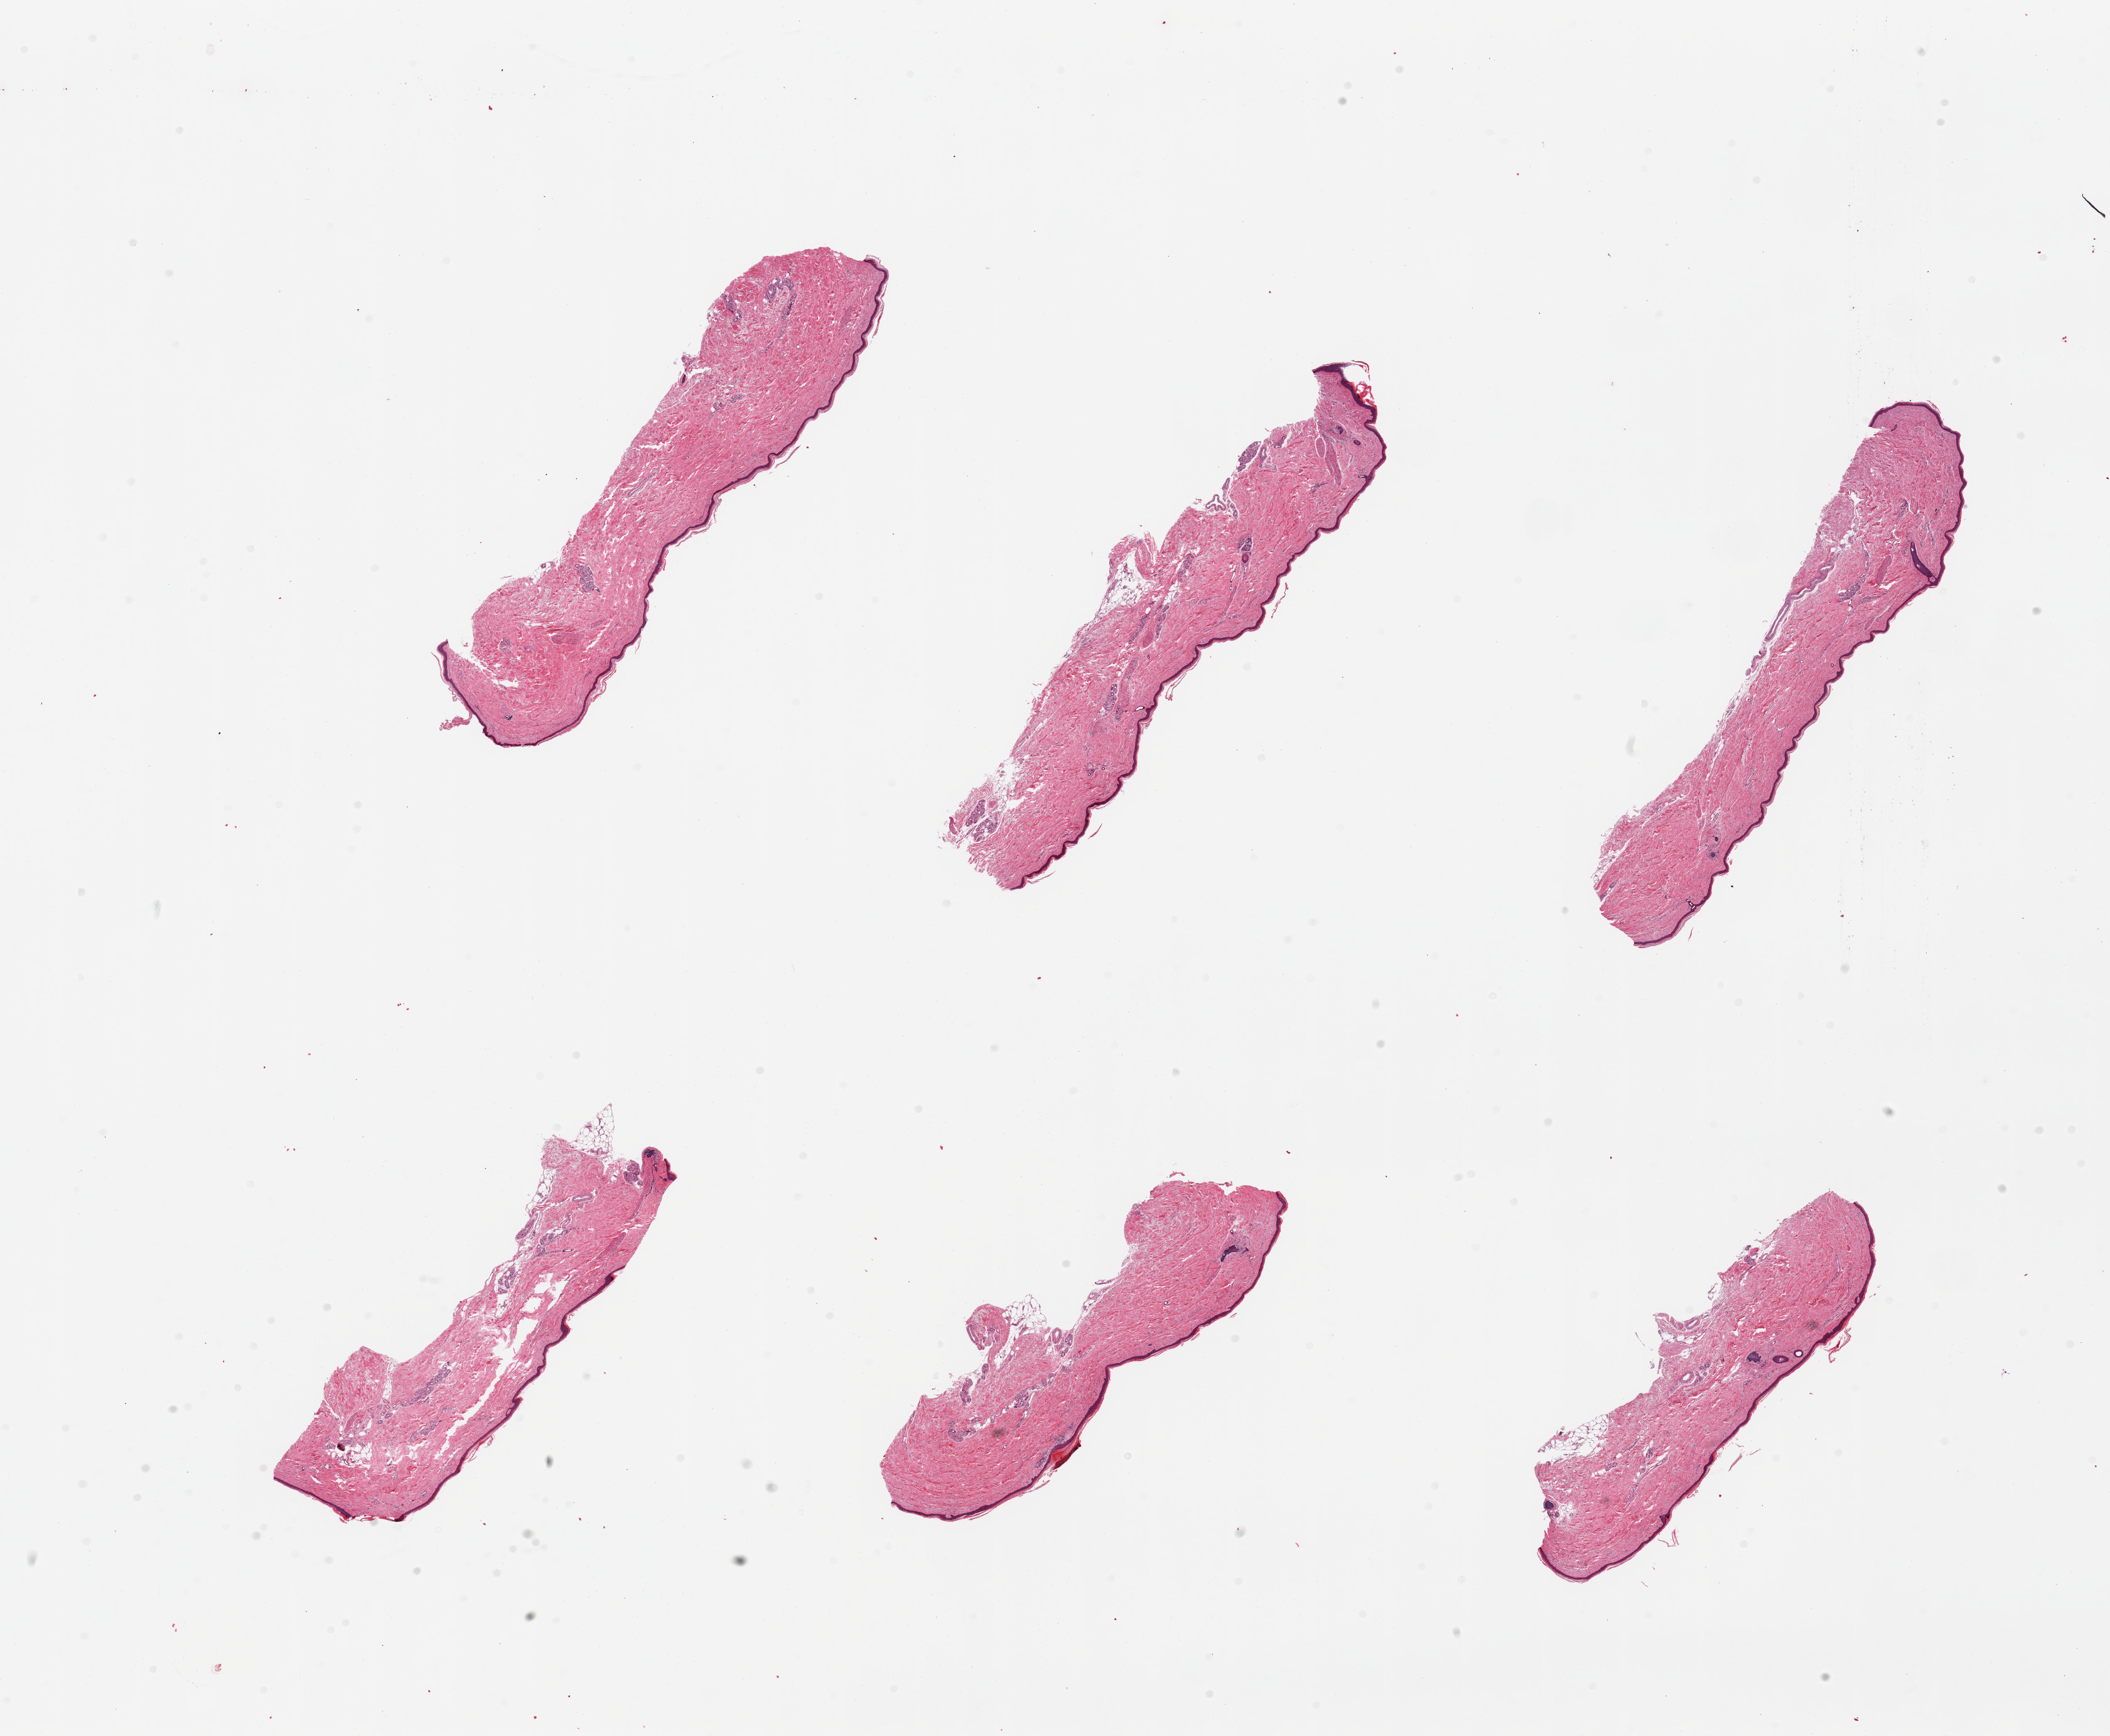
Digitized hematoxylin and eosin (H&E)-stained section — a low-resolution overview of the entire scanned area, about 26.6 x 21.9 mm. PAXgene-fixed, paraffin-embedded tissue. Sampled site (target tissue): skin of lower leg. Donor tissue sample. Donor sex: female.
Review note (as recorded): 6 pieces, minimal fat, squamous epithelium is ~30 microns.